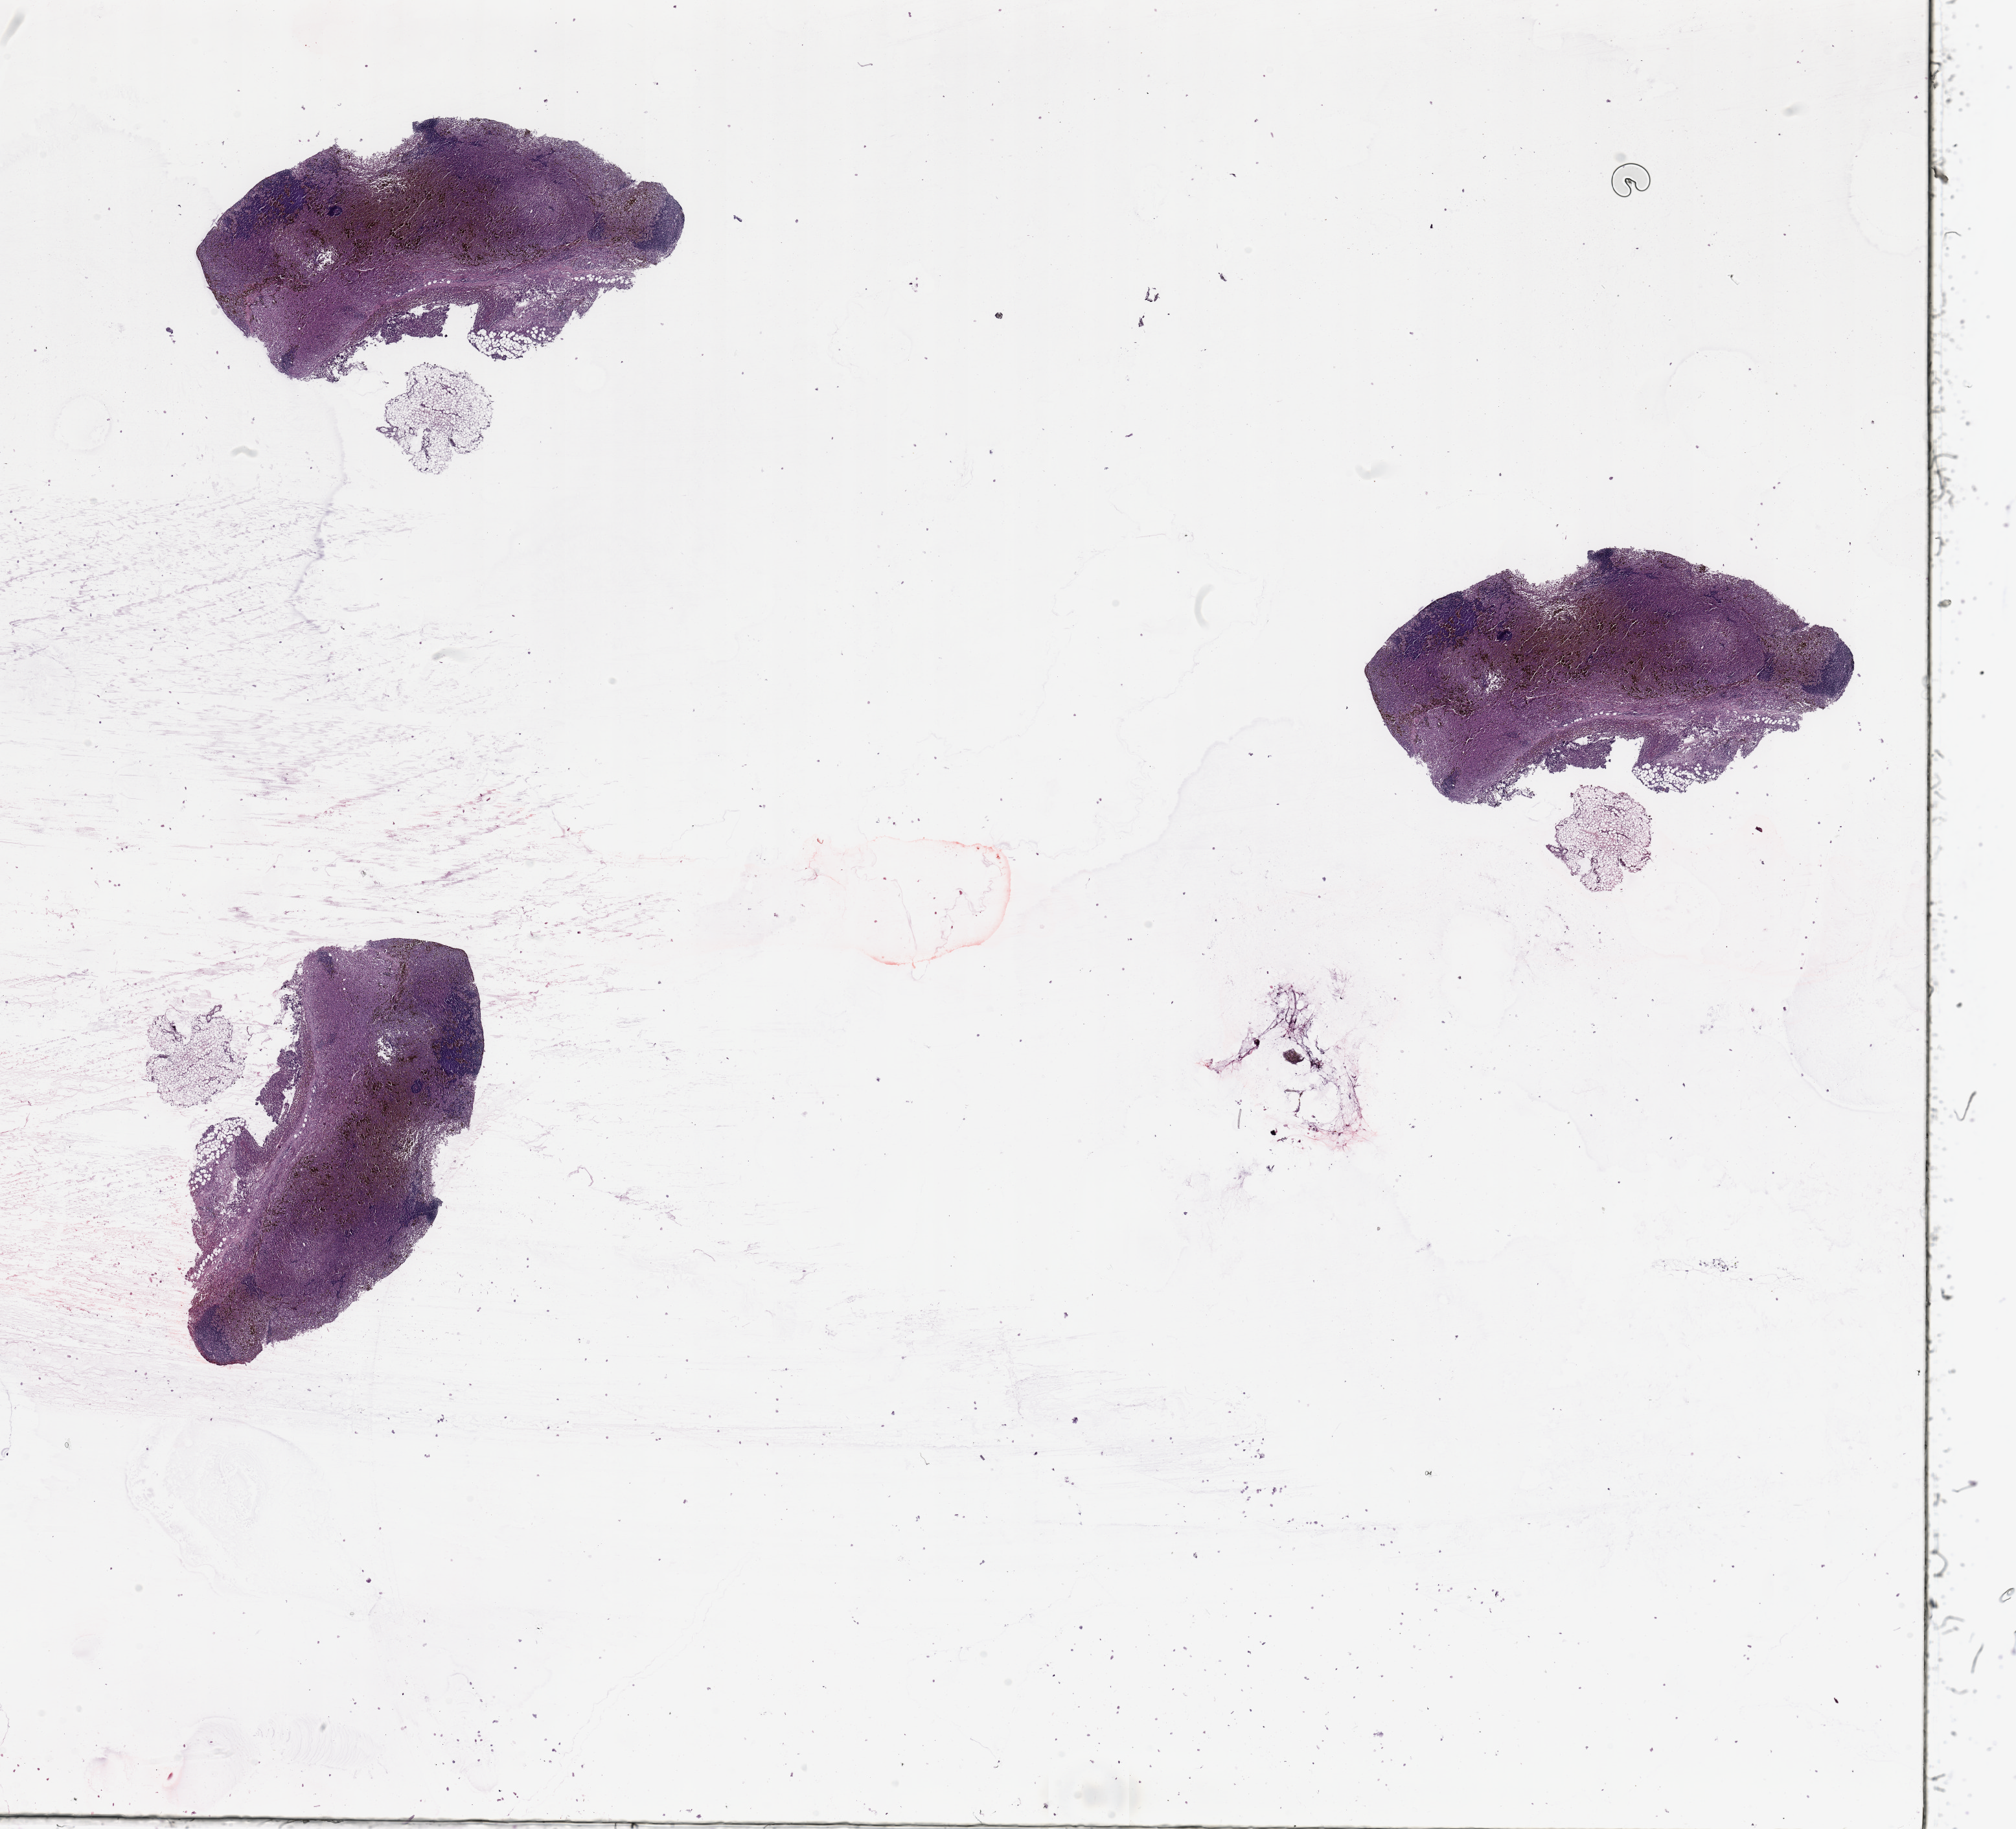
Digitized H&E-stained tissue section (whole slide) — shown as a low-resolution overview of the whole scanned area (about 24.6 x 22.3 mm, acquisition: 20x scan), tumour tissue sample, sampled site: trunk. 51-year-old female patient. Pathologist review of this section (percent, as recorded): tumour nuclei 90%, necrosis 2%.
This section: metastatic tumour tissue. Patient diagnosis: Malignant melanoma, NOS.